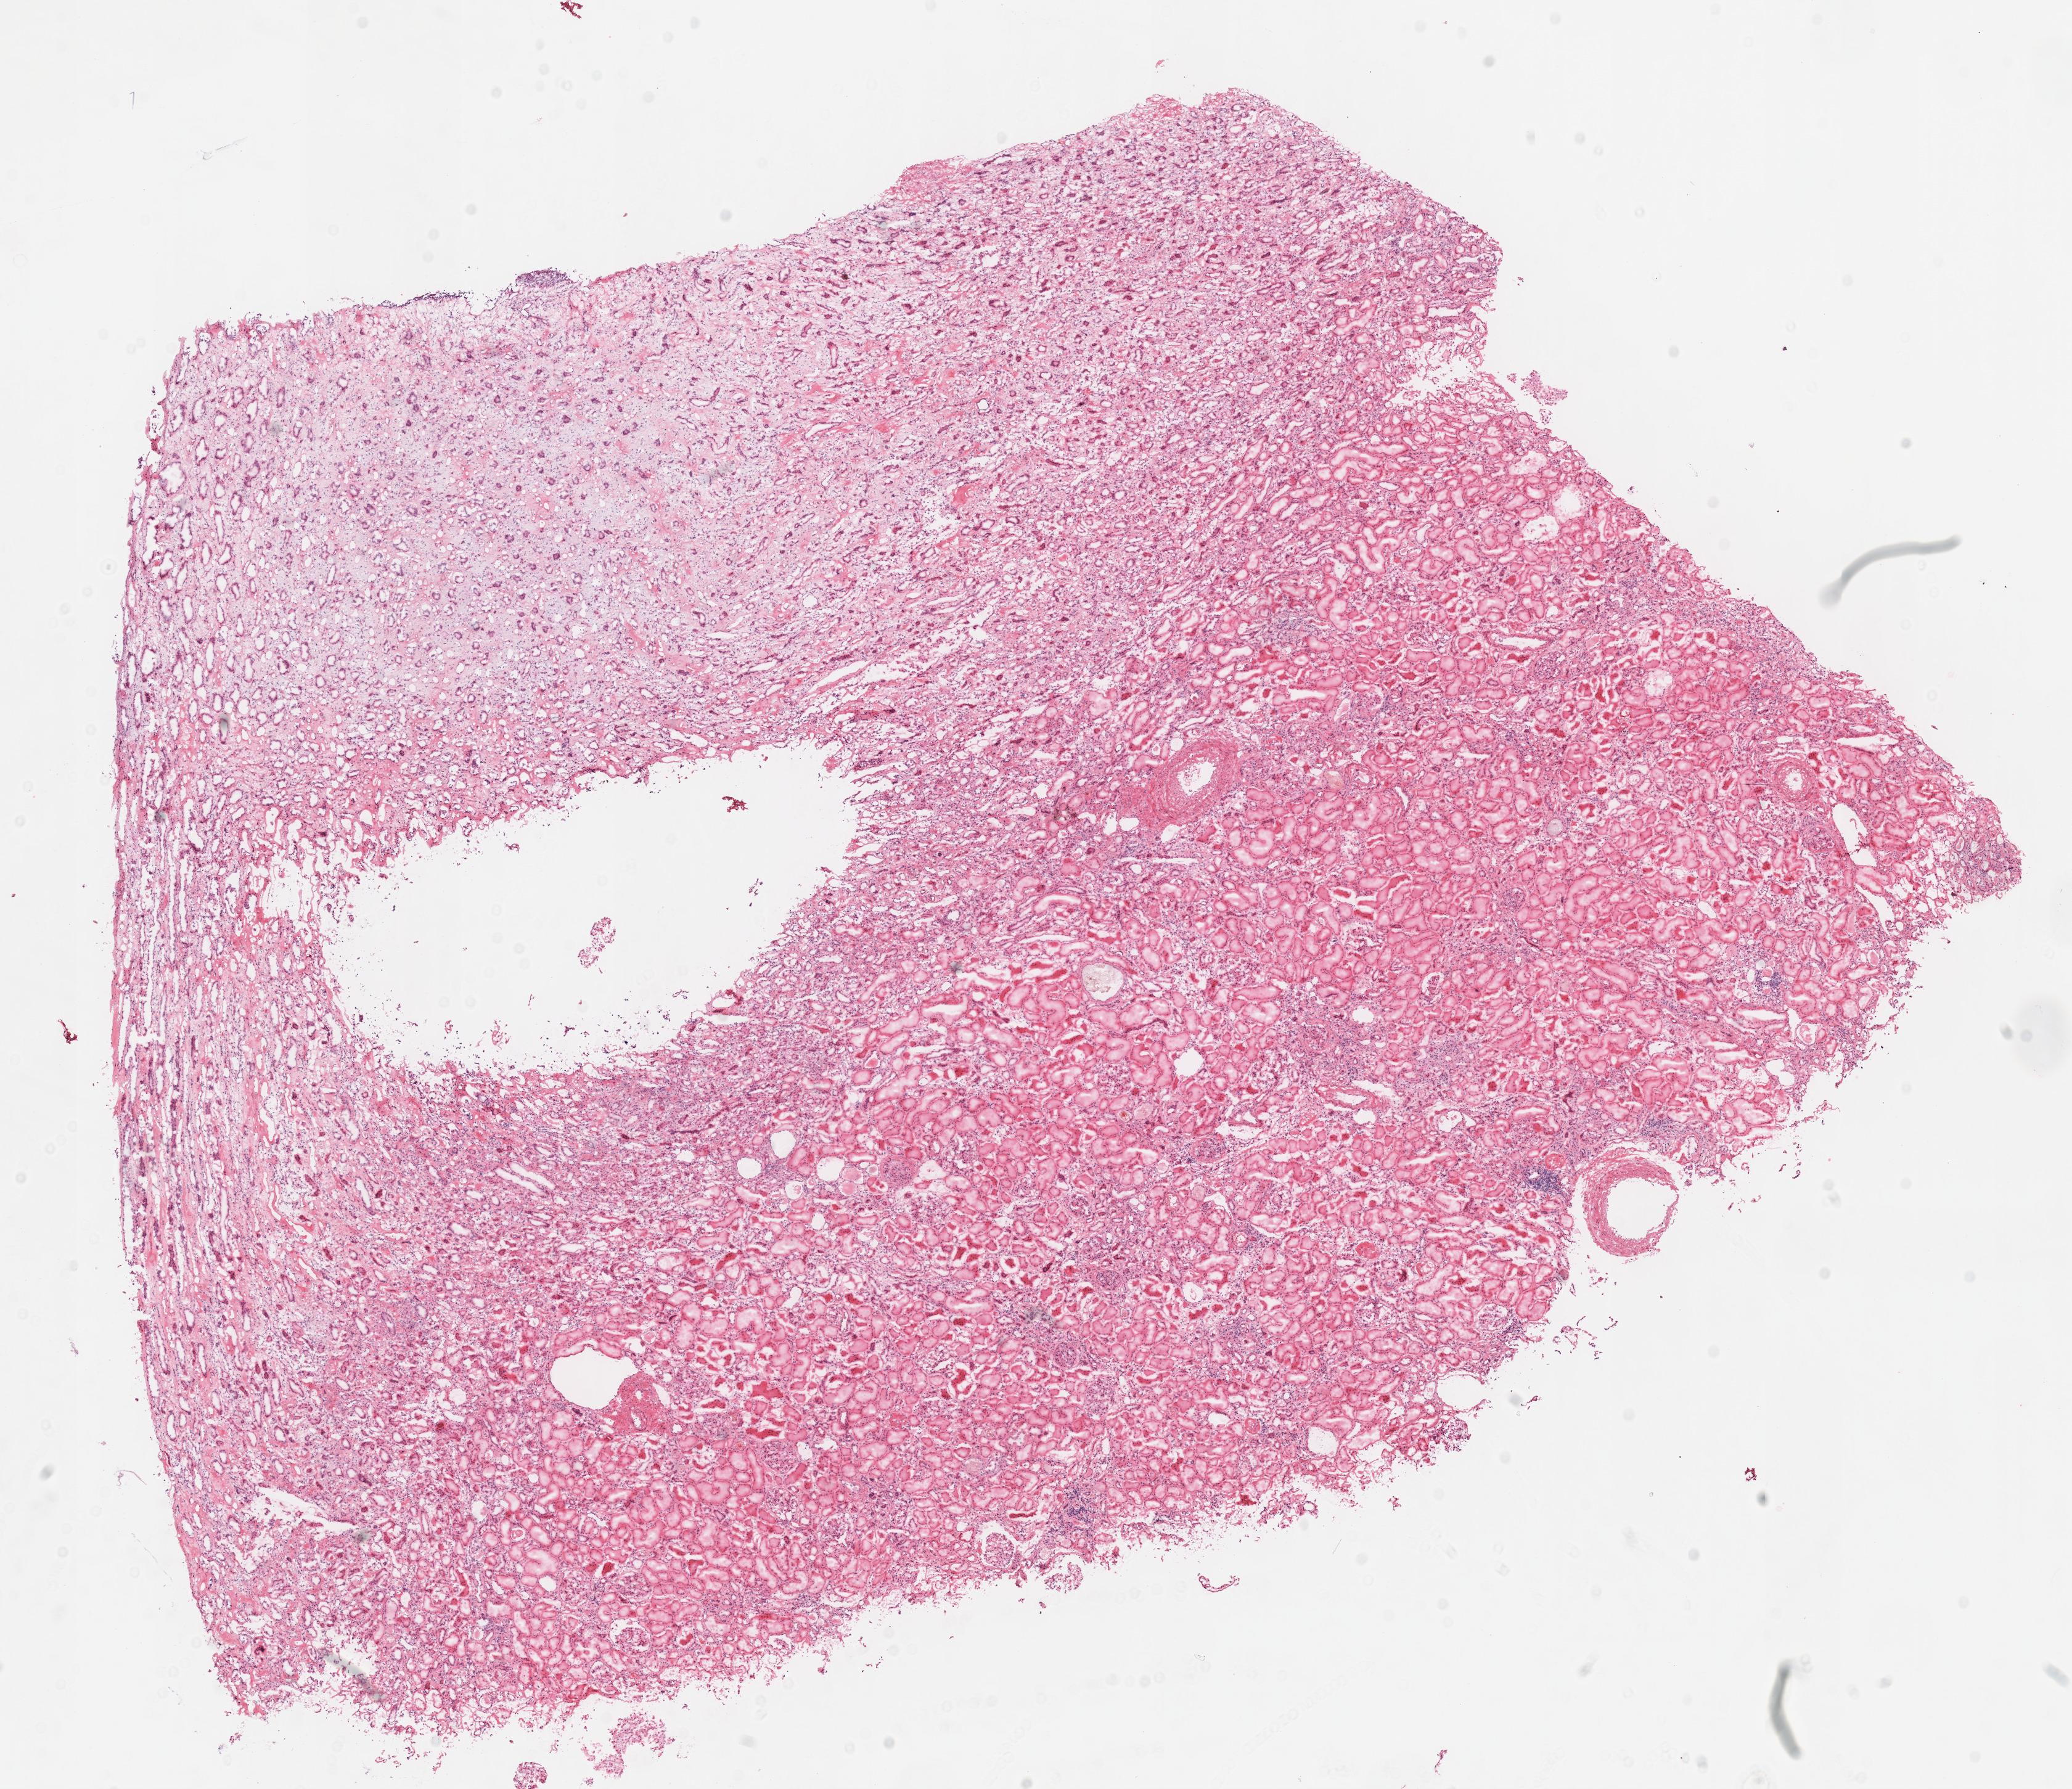
Whole-slide histology image, H&E-stained, a low-resolution overview of the entire scanned area, about 13.2 x 11.4 mm. Frozen section from the top of the tissue portion. Solid tissue normal (non-tumour tissue) sample from the kidney. Male, age 59 years at initial diagnosis. Infiltration values recorded for this section: lymphocyte infiltration 0%, monocyte infiltration 0%, neutrophil infiltration 0%.
This section: solid tissue normal sample (biorepository sample class). Patient diagnosis: Renal cell carcinoma, chromophobe type.